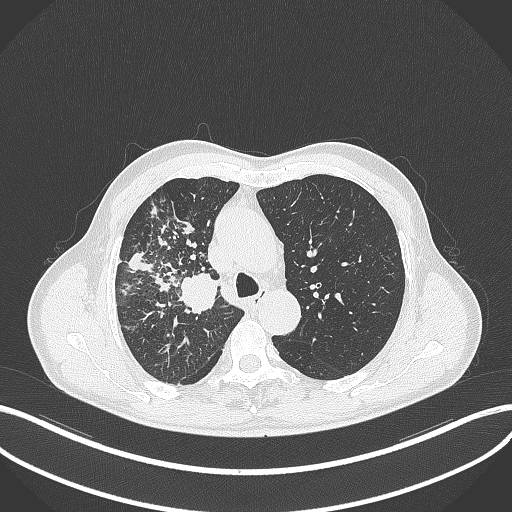
Chest CT, one axial slice. Slice 341 of 490 in the series (ordered by position). Reconstruction kernel B70f. Lung window (W 1500 / L -600 HU). 1 mm slice thickness. 512 × 512 image matrix, field of view 400 × 400 mm. Patient: male, 69 years. From the clinical record (not read from this slice): clinical TNM (as recorded): T2a N0 M0.
Structures marked on this image (bounding box drawn by a radiologist):
- lung tumour (recorded histology: adenocarcinoma): bounding box <176,272,219,314> (left, top, right, bottom; pixels)